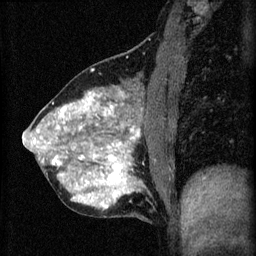
Breast MRI (dynamic contrast-enhanced), one sagittal slice. Slice 25 of 60 in the series (ordered by position). 3 images stored at this slice position (order not interpretable as contrast timing). 1.5 T. TE 4.2 ms, TR 8.2 ms. 2 mm slice thickness. 256 × 256 image matrix. Patient: female, 40 years.
Structures marked on this image (semi-automatic segmentation, software-assisted and operator-edited):
- analysis volume of interest (the breast-tissue region the enhancement analysis was run in; not a lesion): box from (x=24, y=76) to (x=175, y=219) px
- tumour enhancement mask (voxels above the 70 % enhancement threshold inside the analysis volume of interest): (x=24, y=92)–(x=141, y=209)